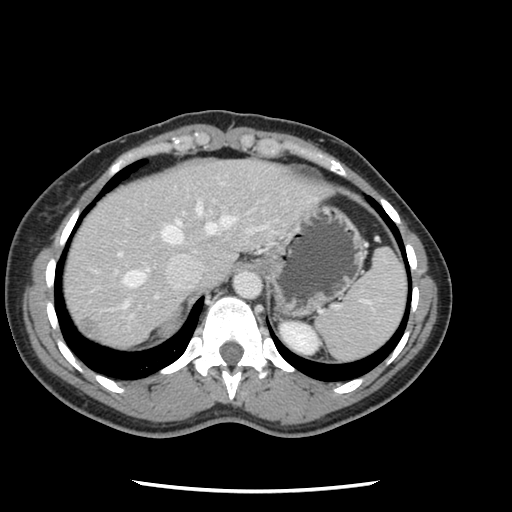
Contrast-enhanced abdominal CT, one axial slice. Position 98 of 134 along the scan axis. 120 kVp. Intravenous contrast given. Soft-tissue window (W 400 / L 40 HU). 2.5 mm slice thickness. 512 × 512 image matrix, field of view 330 × 330 mm. Female patient, age 43 years. Case-level facts recorded for this patient, not image findings: diagnosis: colorectal cancer liver metastases, imaged before liver resection; multiple liver metastases: yes; largest metastasis: 3.4 cm; chemotherapy before resection: no.
Structures marked on this image (manually delineated by an expert):
- hepatic veins: bounding box [x1, y1, x2, y2] px = [122, 202, 237, 309]
- liver: [64, 160, 326, 349]
- planned liver remnant (the part of the liver to remain after resection): [63, 170, 196, 307]
- portal vein (with intrahepatic branches): [117, 218, 268, 319]
- liver metastasis: [76, 319, 100, 341]